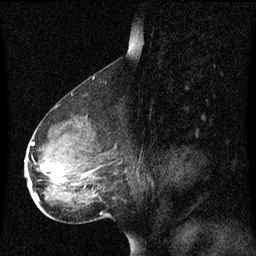
Breast MRI (dynamic contrast-enhanced), one sagittal slice; position 41 of 60 along the scan axis; dynamic contrast-enhanced series, image 2 of 3 at this slice position (ordered by acquisition); 1.5 T; TE 4.2 ms, TR 8.4 ms; 2 mm slice thickness; 256 × 256 image matrix. Patient: female, 49 years. From the clinical record (not read from this slice): setting: breast cancer imaged before/during neoadjuvant chemotherapy; receptor status: HR-positive, HER2-negative.
Annotated regions visible in this slice (semi-automatically segmented with operator editing):
- analysis volume of interest (the breast-tissue region the enhancement analysis was run in; not a lesion): bounding box <26,126,118,201> (left, top, right, bottom; pixels)
- tumour enhancement mask (voxels above the 70 % enhancement threshold inside the analysis volume of interest): <30,142,65,201>